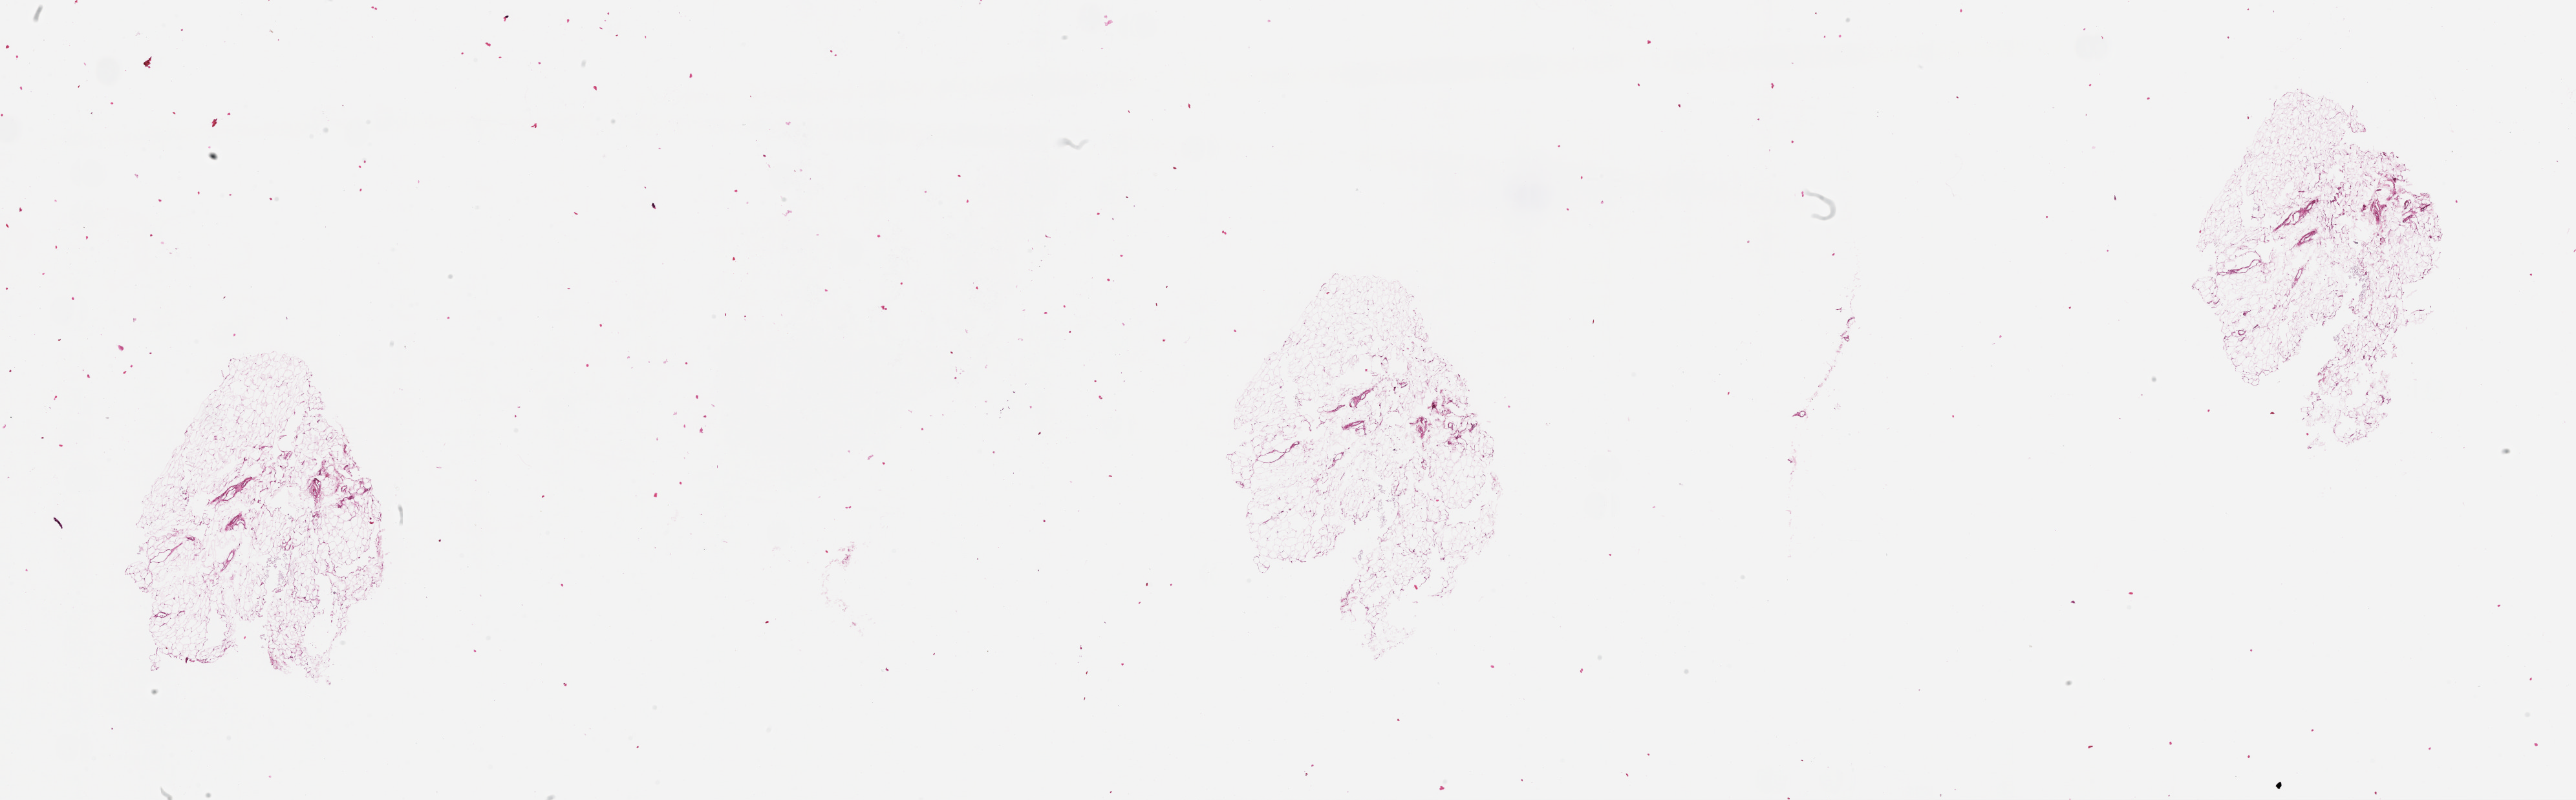
H&E whole-slide image, whole scanned area (about 32.1 x 10.0 mm, acquisition: 20x scan) shown as a low-resolution overview. Male, 57 y/o.
• patient diagnosis: Malignant melanoma, NOS